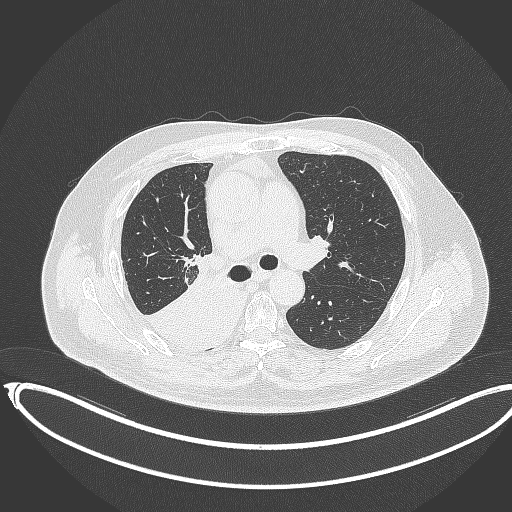
Chest CT, one axial slice; slice 224 of 403 in the series (ordered by position); reconstruction kernel B70f; lung window (W 1500 / L -600 HU); 512 × 512 image matrix, field of view 436 × 436 mm. Patient: male, 68 years. From the clinical record (not read from this slice): clinical TNM (as recorded): T2a N0 M0.
Outlined on this slice (rectangle marked by the reading radiologist):
- lung tumour (recorded histology: adenocarcinoma): bounding box [x1, y1, x2, y2] px = [137, 255, 237, 351]